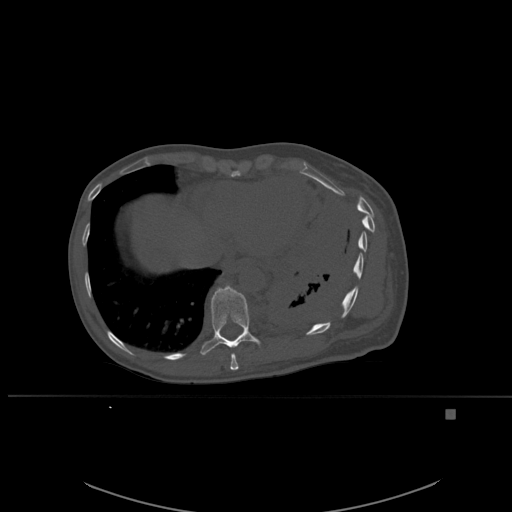
CT including the spine, one axial slice. Slice 319 of 537 in the series (ordered by position). Bone window (W 1800 / L 400 HU). 1.5 mm slice thickness. 512 × 512 image matrix, field of view 440 × 440 mm. Female patient, age 45 years. From the clinical record (not read from this slice): primary cancer: lung.
Outlined on this slice (semi-automatic segmentation, software-assisted and operator-edited):
- T10 vertebra: bounding box (x1, y1, x2, y2) in pixels: (200, 284, 261, 356)
- T9 vertebra: (230, 353, 239, 370)